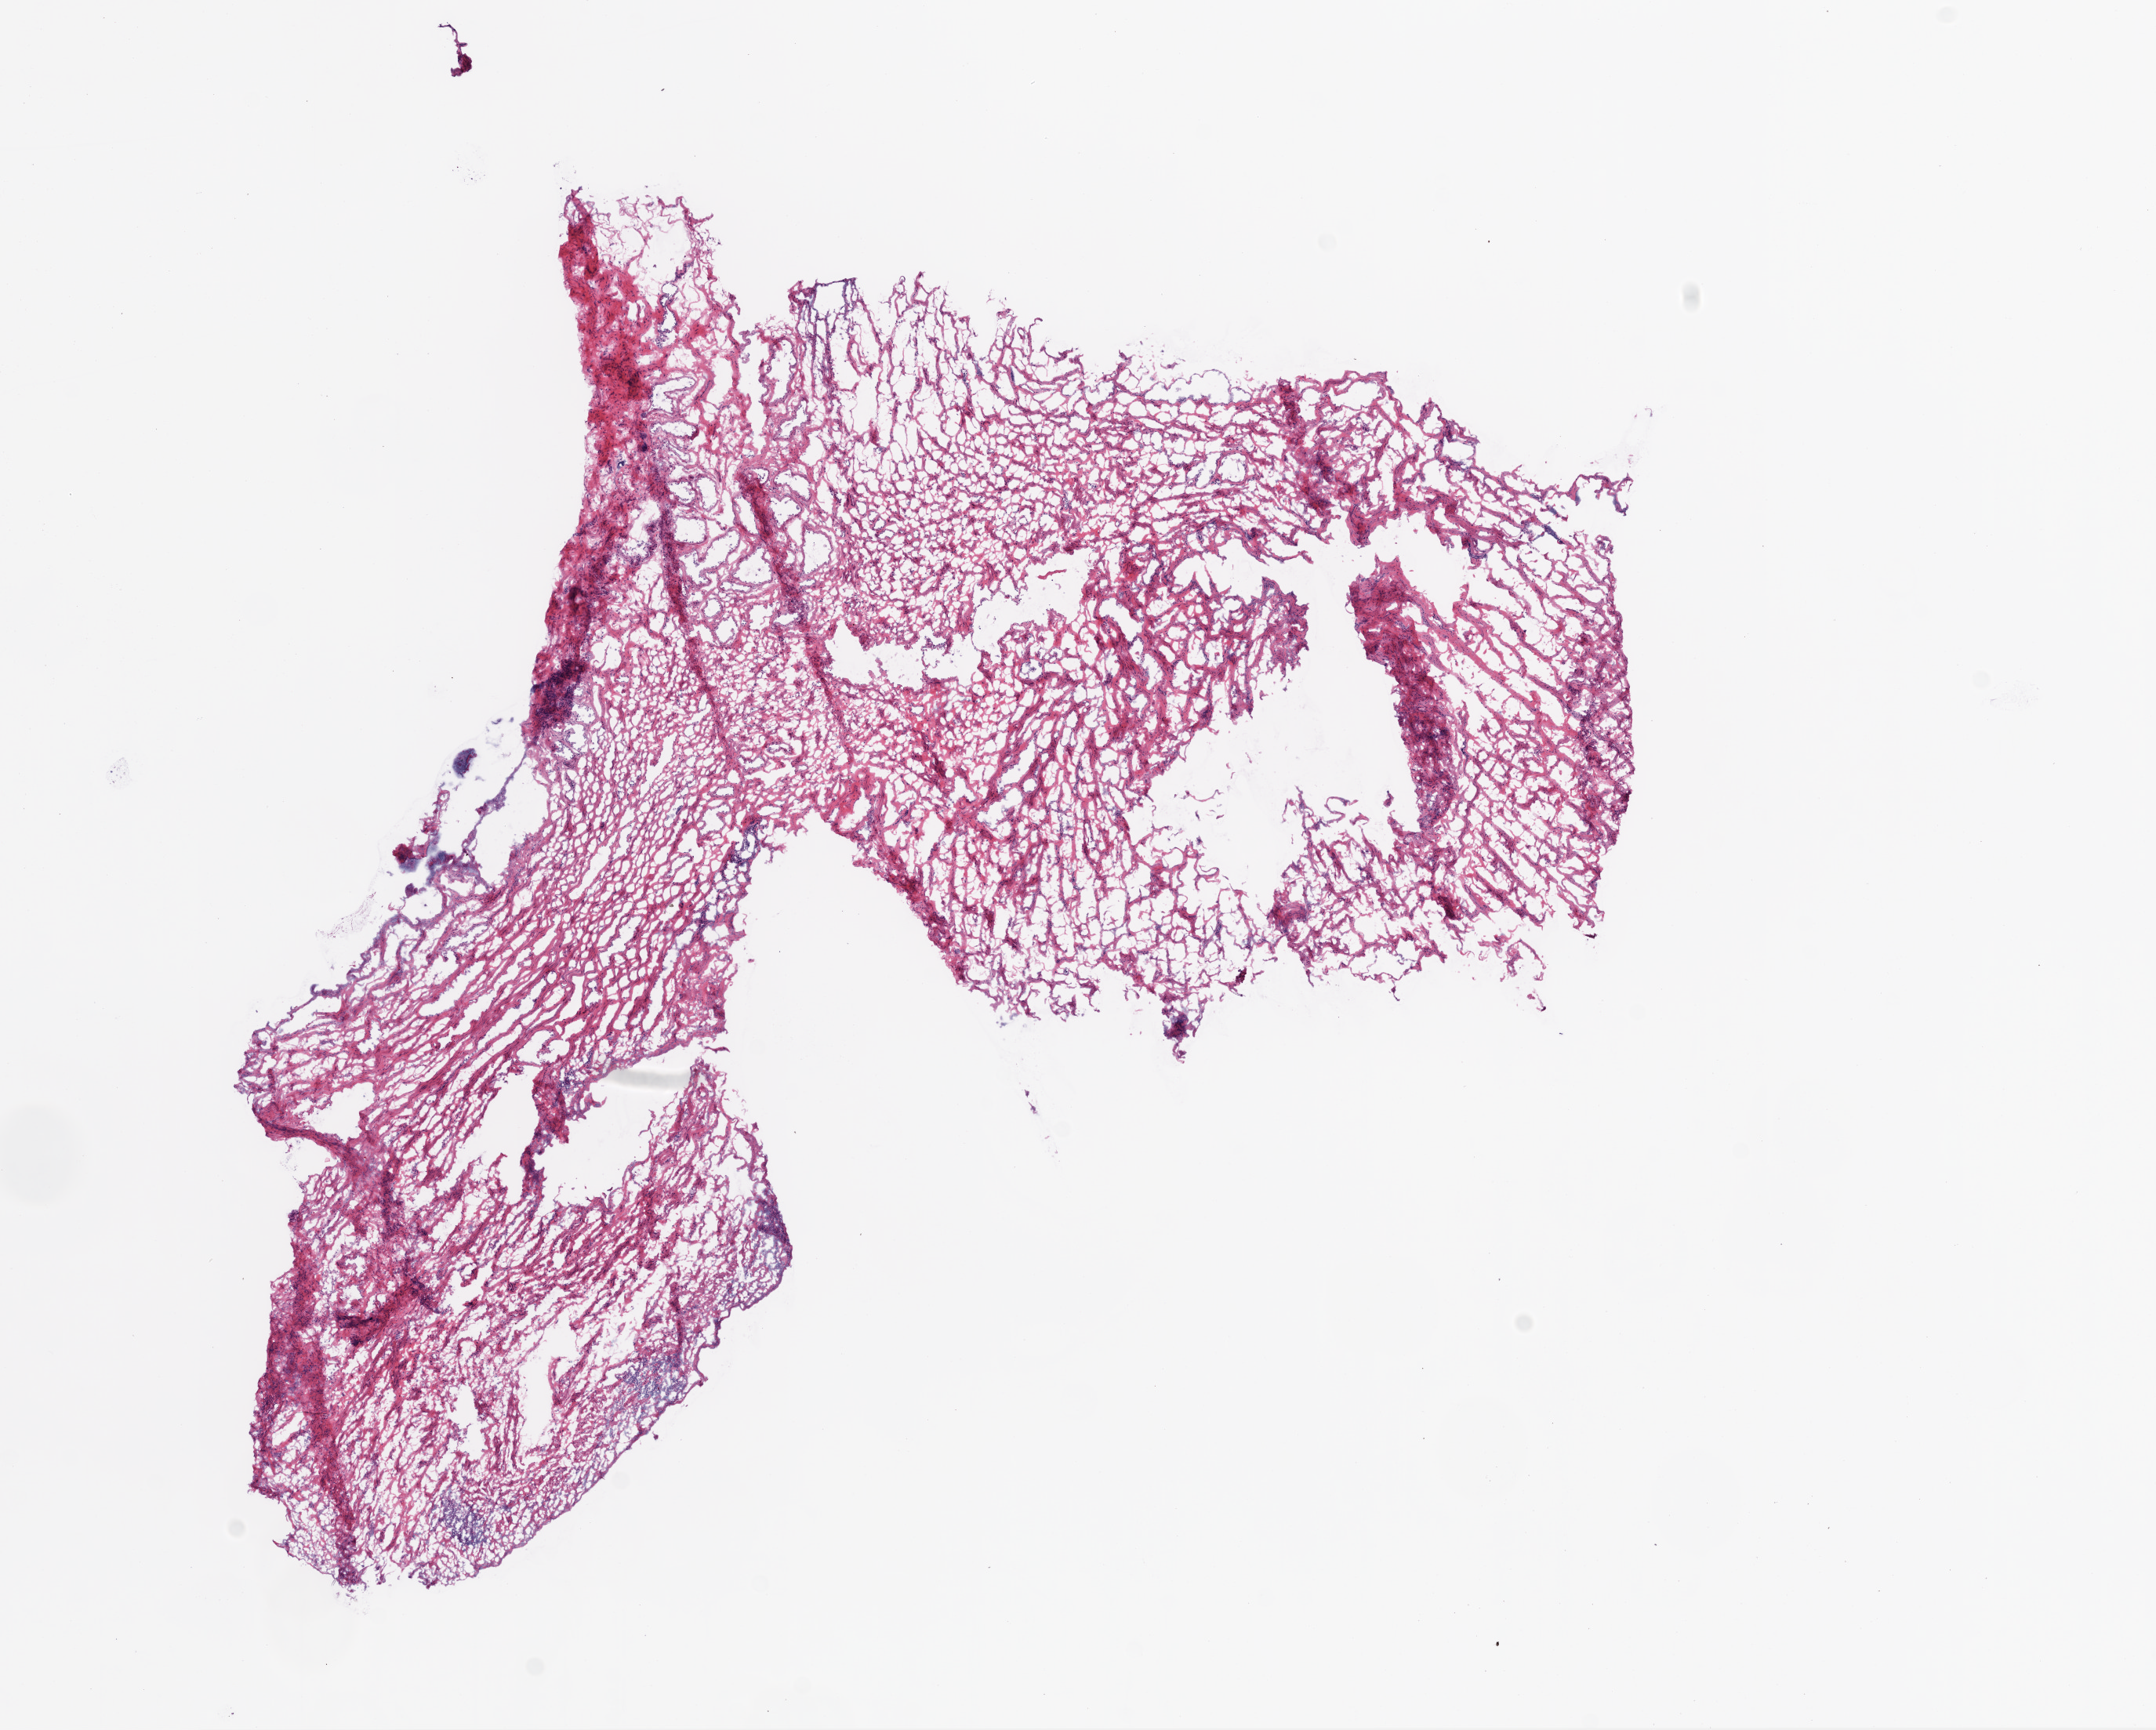
Hematoxylin and eosin (H&E) stained whole-slide image — a low-resolution overview of the entire scanned area, about 11.0 x 8.9 mm, frozen section, ovary, solid tissue normal (non-tumour tissue) sample. Patient: female, age at initial diagnosis 44 years.
This section: solid tissue normal sample (biorepository sample class). Patient diagnosis: Serous cystadenocarcinoma, NOS.